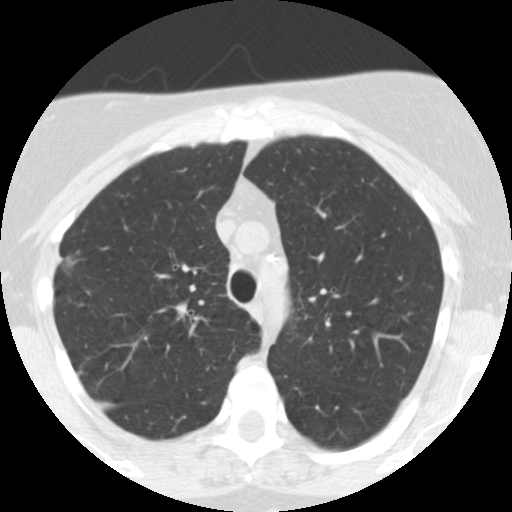
Low-dose screening chest CT, one axial slice; position 185 of 248 along the scan axis; reconstruction kernel STANDARD; 120 kVp; lung window (W 1500 / L -600 HU); 2.5 mm slice thickness; 512 × 512 image matrix, field of view 287 × 287 mm.
Structures marked on this image (outlined manually by an expert reader):
- lesion 1 (tumor, upper lobe of right lung): bounding box <67,257,74,264> (left, top, right, bottom; pixels)